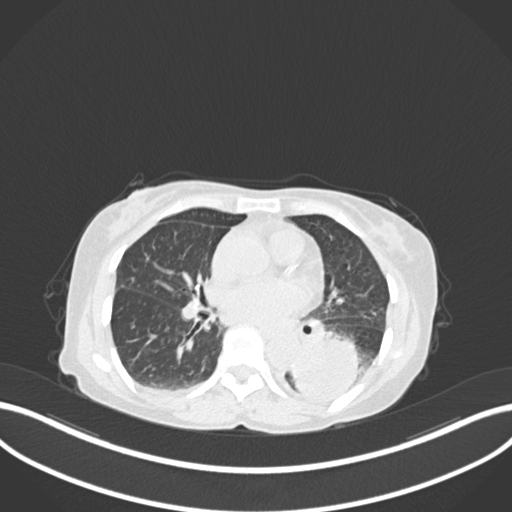
Chest CT, one axial slice. Slice 72 of 233 in the series (ordered by position). 120 kVp. Lung window (W 1500 / L -600 HU). 1 mm slice thickness. 512 × 512 image matrix, field of view 400 × 400 mm. Patient: female, 78 years. From the clinical record (not read from this slice): clinical TNM (as recorded): T3 N0 M1.
Structures marked on this image (rectangle marked by the reading radiologist):
- lung tumour (recorded histology: squamous cell carcinoma): bounding box (x1, y1, x2, y2) in pixels: (287, 328, 366, 400)